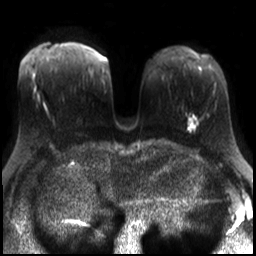
Breast MRI, one axial slice. Slice 13 of 30 in the series (ordered by position). Diffusion-weighted series; image 2 of 4 stored at this slice position (different b-values; order by instance number). 3 T. 4 mm slice thickness. 256 × 256 image matrix. Female patient.
Structures marked on this image (outlined manually by an expert reader):
- tumour on diffusion-weighted imaging: bounding box <188,119,194,130> (left, top, right, bottom; pixels)